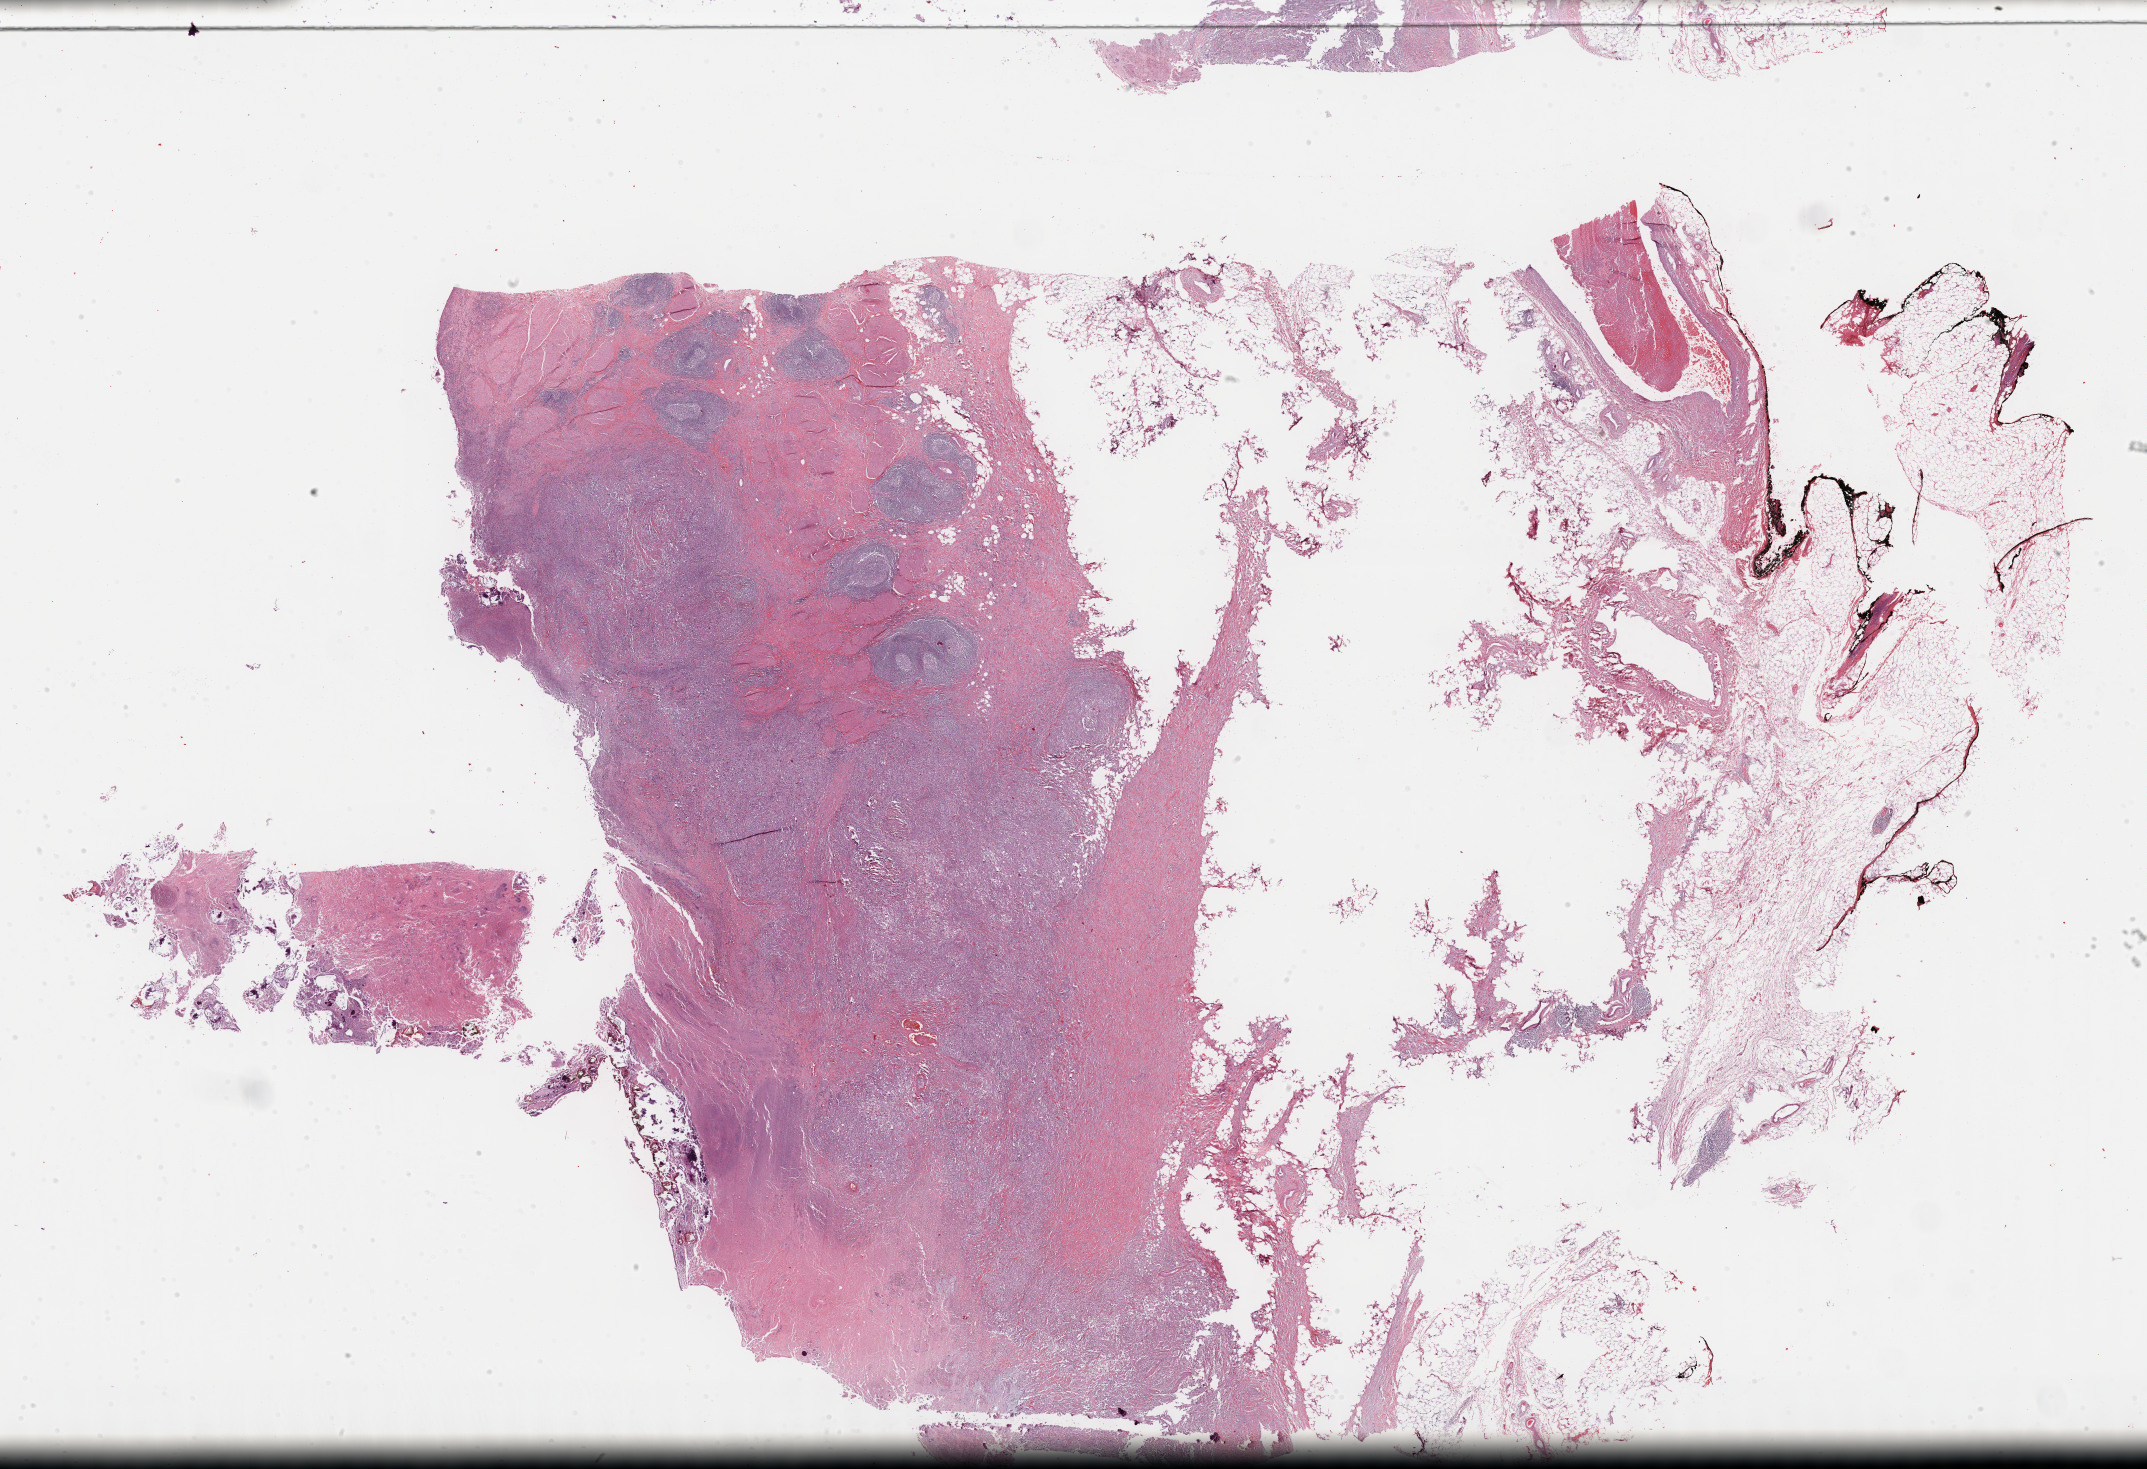
Whole-slide histology image, H&E, low-resolution overview of the scanned area, about 34.7 x 23.8 mm, formalin-fixed paraffin-embedded (FFPE) diagnostic section, bladder, primary tumour sample. Female patient; age at initial diagnosis 60 years. Histologic grade: high grade.
- histologic diagnosis: Transitional cell carcinoma
- AJCC pathologic stage: IV (6th edition)
- TNM: T3b N2 MX